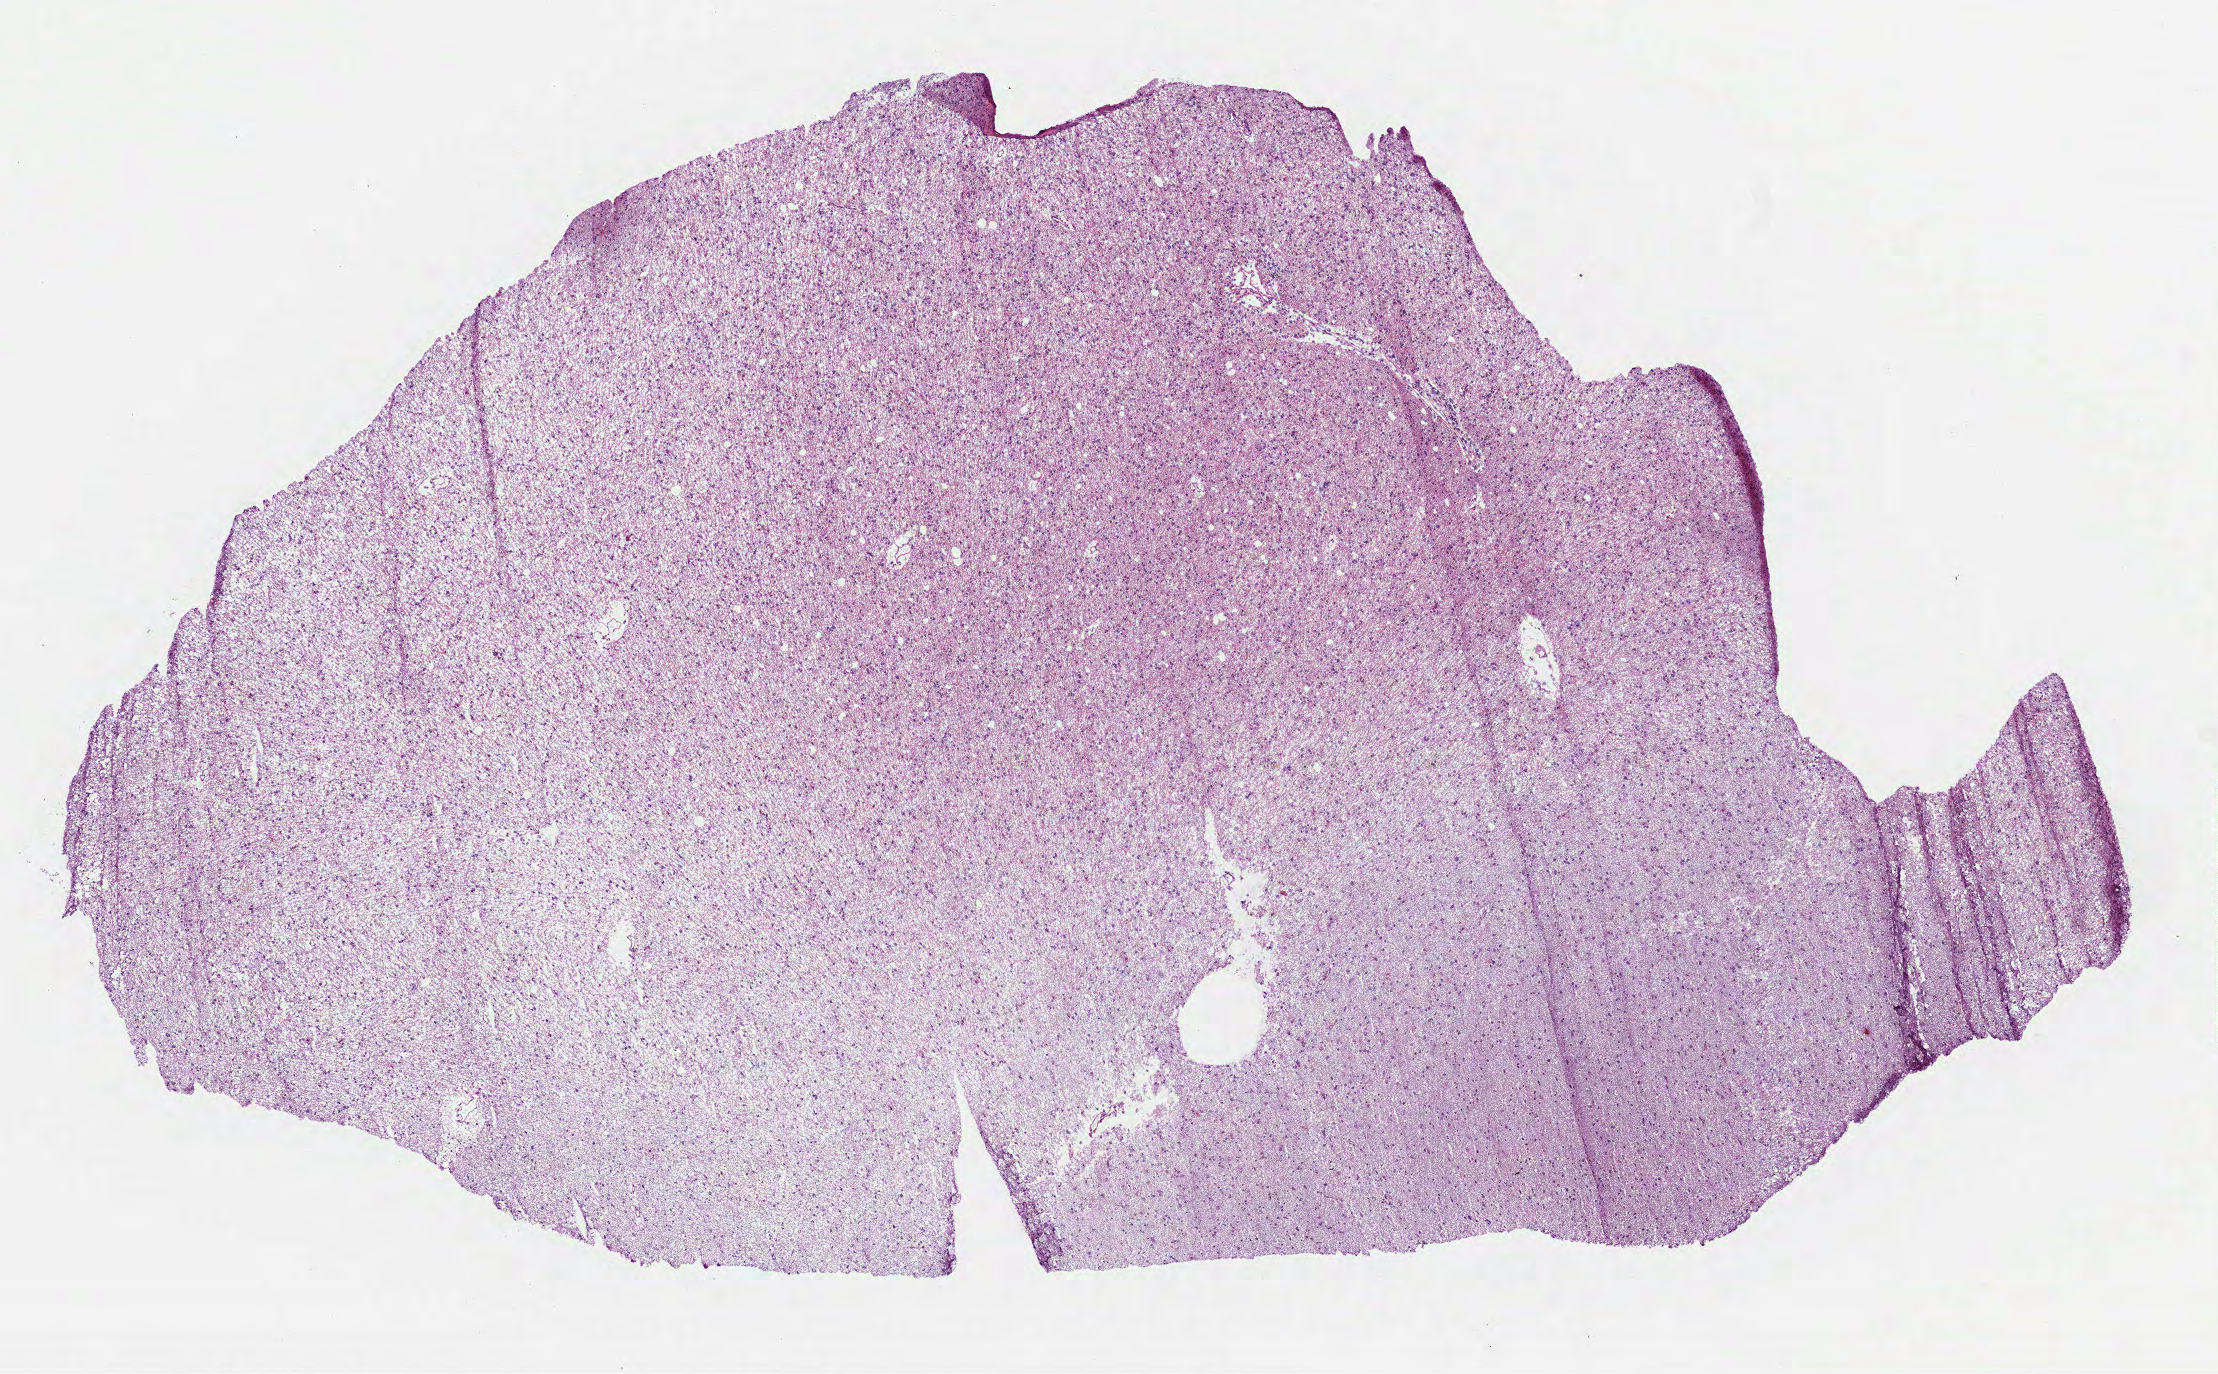
Digitized H&E-stained tissue section (whole slide), whole scanned area (about 8.9 x 5.5 mm) shown as a low-resolution overview, frozen section from the top of the tissue portion, sample: primary tumour, brain. Female, age 38 years at initial diagnosis. Histologic grade: G3 (poorly differentiated). Composition of this section per pathologist review: tumour cells 100%, tumour nuclei 65%, normal cells 0%, stromal cells 0%, necrosis 0%.
* histologic diagnosis: Astrocytoma, anaplastic (cerebrum)